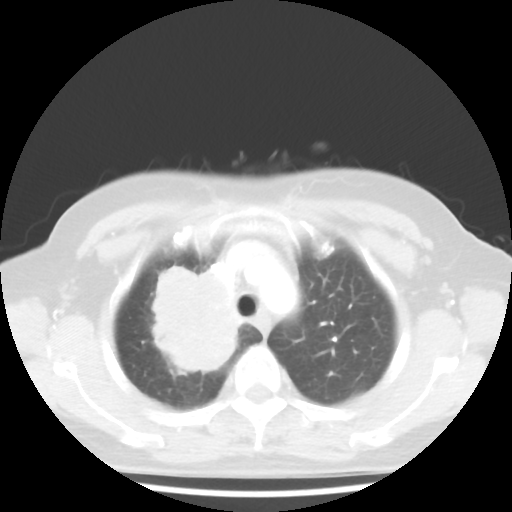
Chest CT, one axial slice; position 35 of 44 along the scan axis; reconstruction kernel STANDARD; 100 kVp; lung window (W 1500 / L -600 HU); 512 × 512 image matrix, field of view 316 × 316 mm. Female patient, age 62 years. Case-level facts recorded for this patient, not image findings: clinical TNM (as recorded): T3 N0 M0; histopathological grade: G3.
Structures marked on this image (rectangle marked by the reading radiologist):
- lung tumour (recorded histology: small cell carcinoma): bounding box (x1, y1, x2, y2) in pixels: (138, 257, 243, 386)